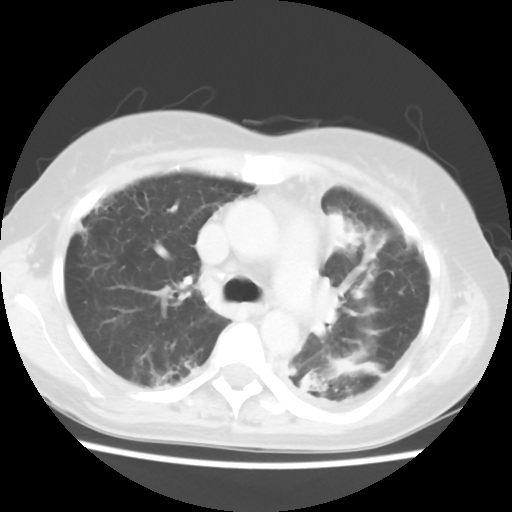
Chest CT, one axial slice. Position 38 of 56 along the scan axis. 120 kVp. Lung window (W 1500 / L -600 HU). 512 × 512 image matrix. Female patient, age 56 years. From the clinical record (not read from this slice): clinical TNM (as recorded): T1c N0 M1.
Outlined on this slice (bounding box drawn by a radiologist):
- lung tumour (recorded histology: adenocarcinoma): bounding box <315,204,356,259> (left, top, right, bottom; pixels)